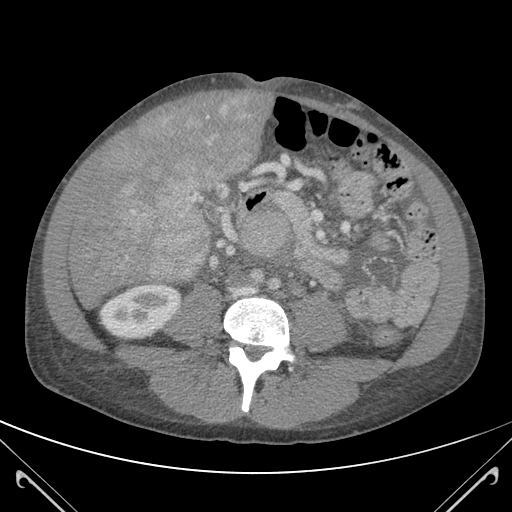
Contrast-enhanced abdominal CT (liver protocol), one axial slice. Position 36 of 118 along the scan axis. 120 kVp. Soft-tissue window (W 400 / L 40 HU). 512 × 512 image matrix, field of view 380 × 380 mm. Case-level facts recorded for this patient, not image findings: diagnosis: hepatocellular carcinoma (patient treated with transarterial chemoembolisation; whether this scan precedes or follows treatment is not stated here); TNM stage (as recorded): Stage-IIIB; Child-Pugh class: A; tumour nodularity: uninodular.
Annotated regions visible in this slice (semi-automatic segmentation, software-assisted and operator-edited):
- mass: box from (x=88, y=92) to (x=259, y=278) px